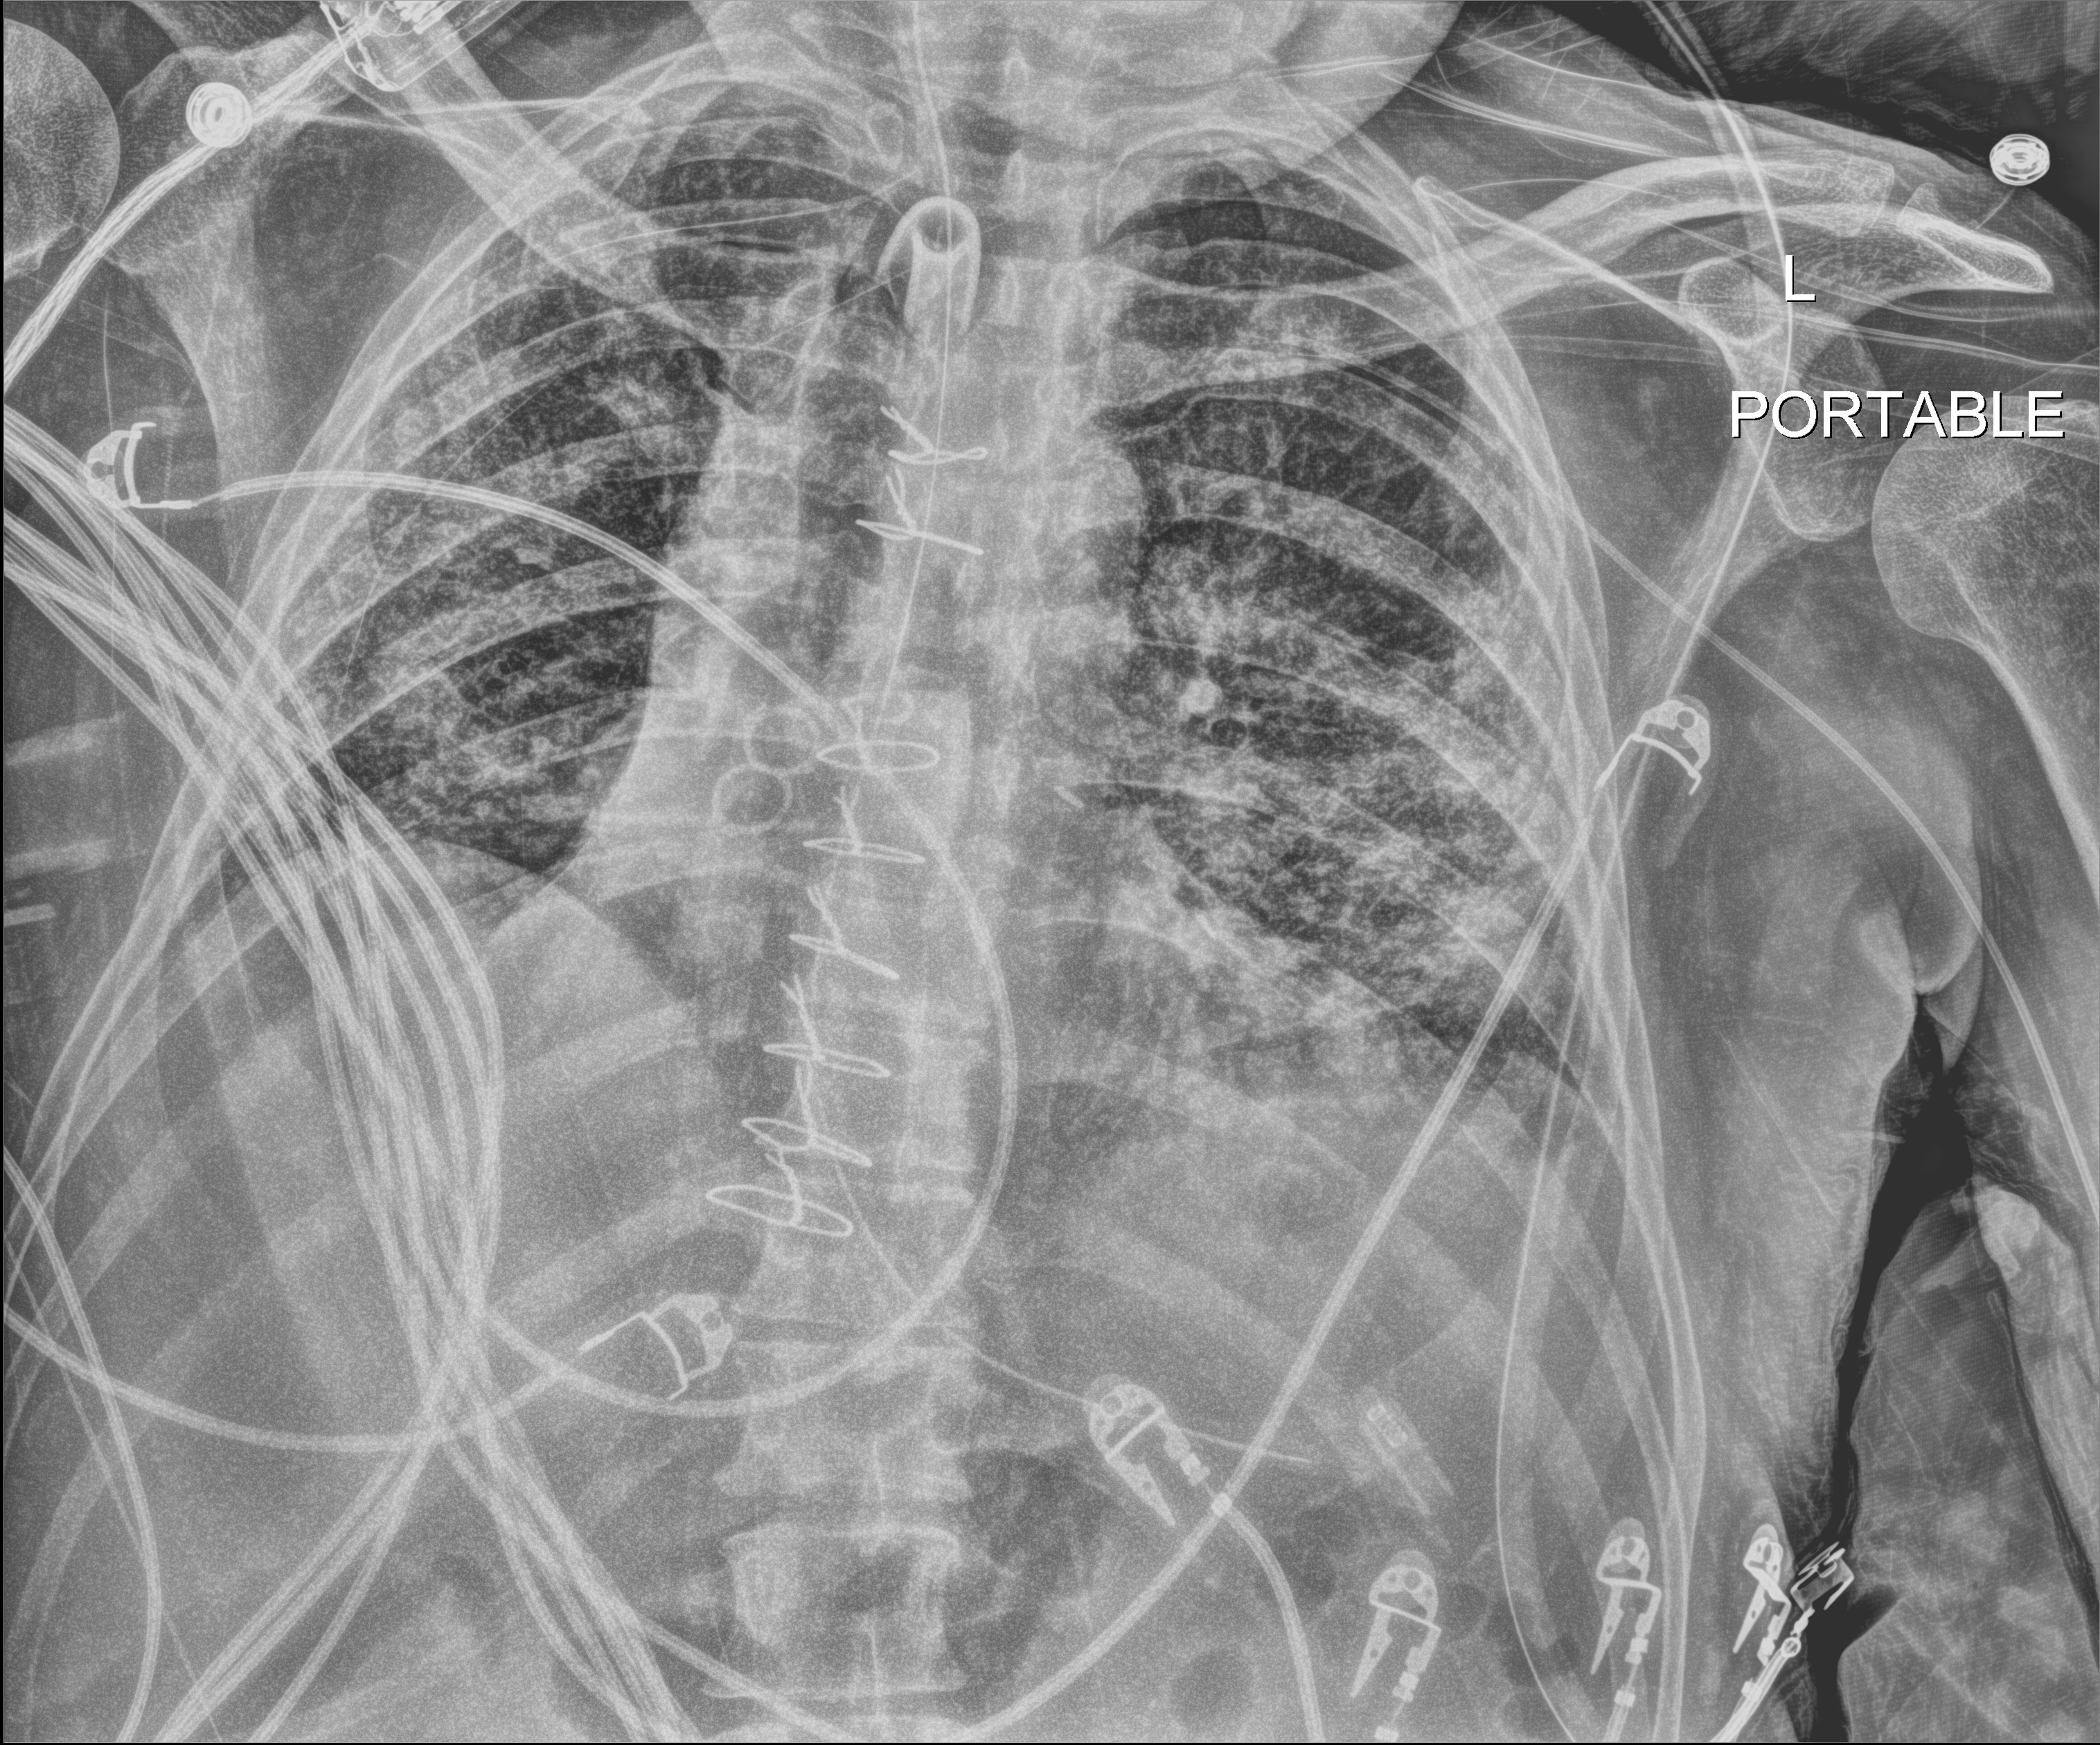
Chest radiograph (digital radiography); anteroposterior (AP) projection. Male patient hospitalised with COVID-19, age 18–59 years.
Hospital-stay facts (about this admission, not read from this image; timing relative to this image not recorded):
- admitted to intensive care during this hospital stay: yes
- COPD (admission record): yes
- mechanically ventilated during this hospital stay: yes